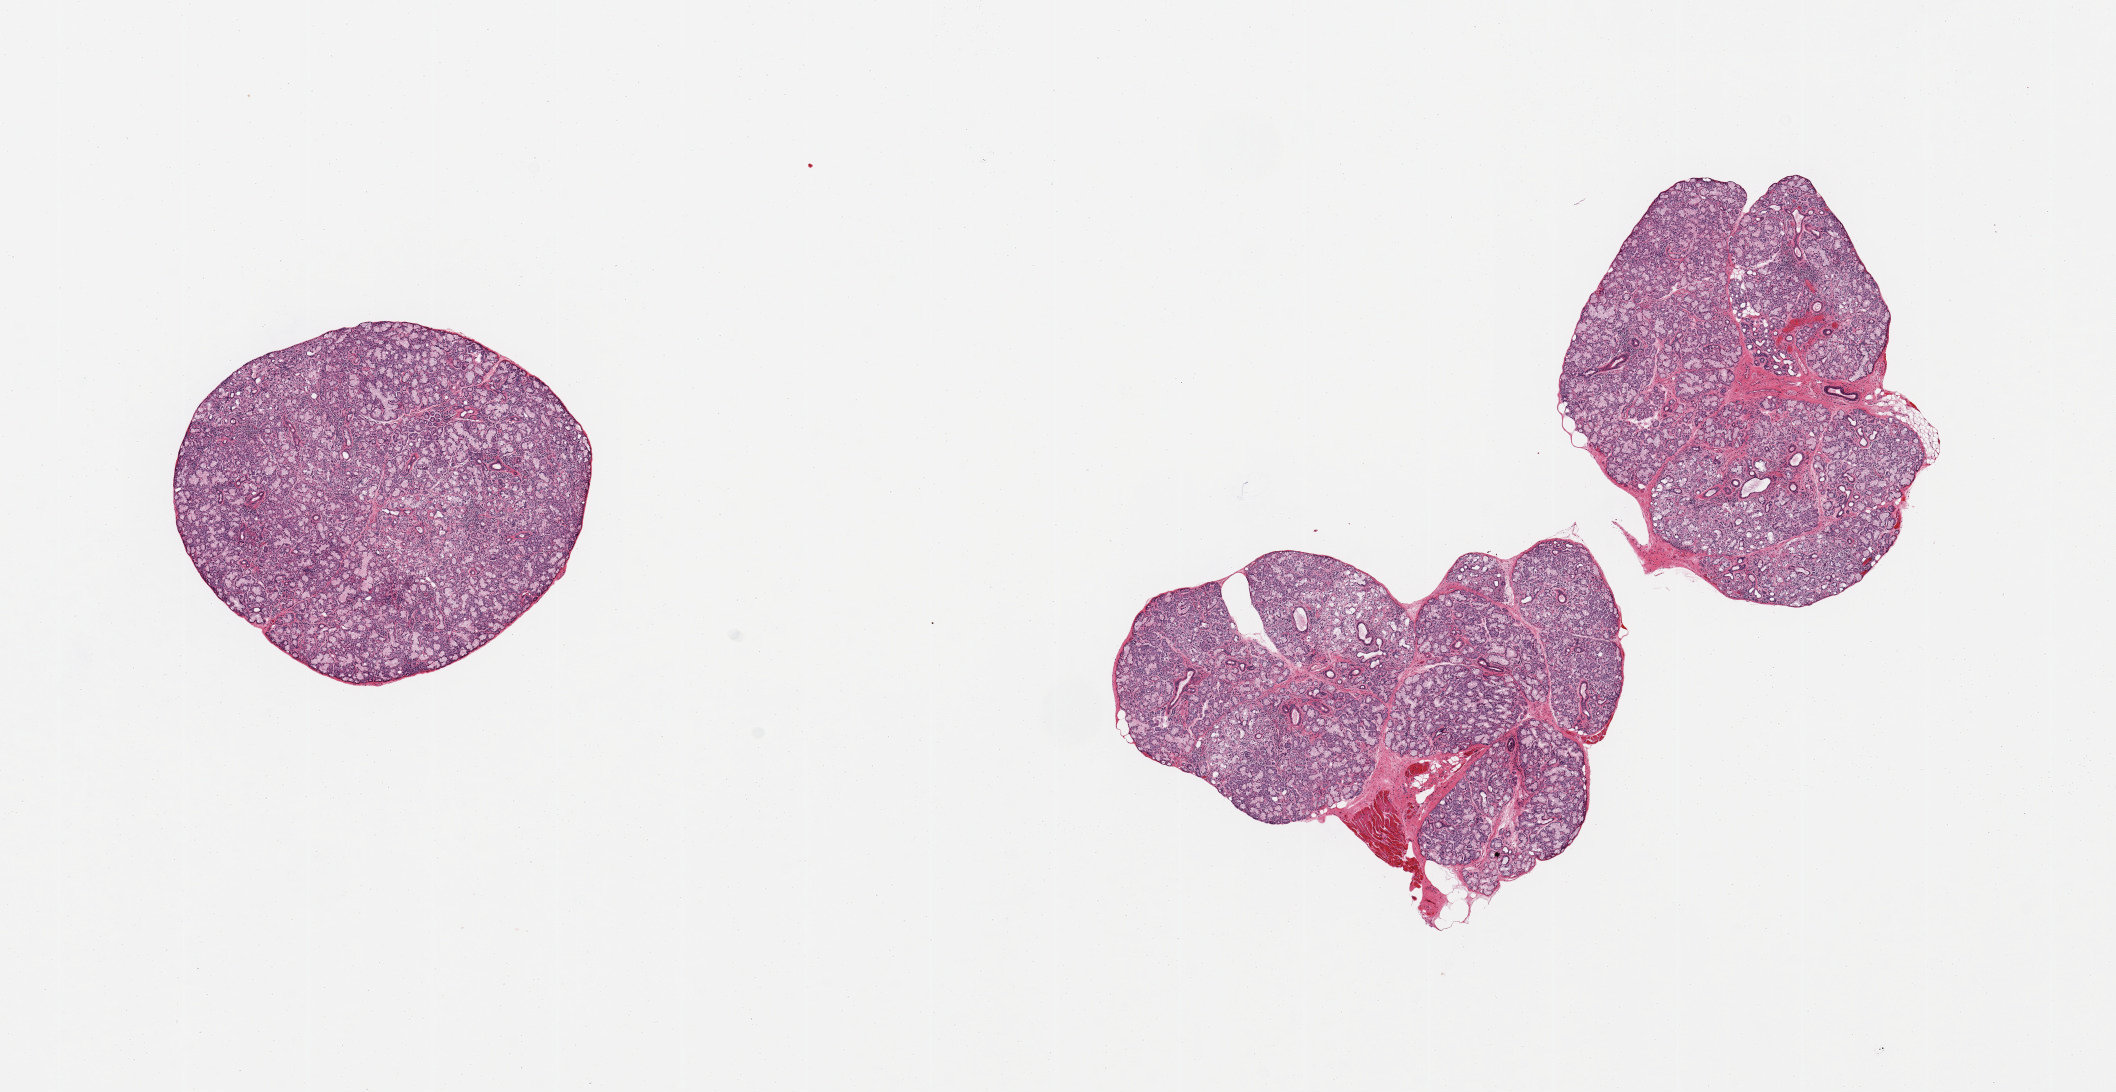
Digitized haematoxylin and eosin-stained section — a low-resolution overview of the entire scanned area, about 16.7 x 8.6 mm. PAXgene-fixed paraffin-embedded (PFPE) section. Target tissue: minor salivary gland. Donor tissue sample. Donor: female.
Pathologist's review note for this sample: 3 pieces; excellent specimen, chronic sialadenitis, trivial attachment of skeletal muscle on 1 piece.